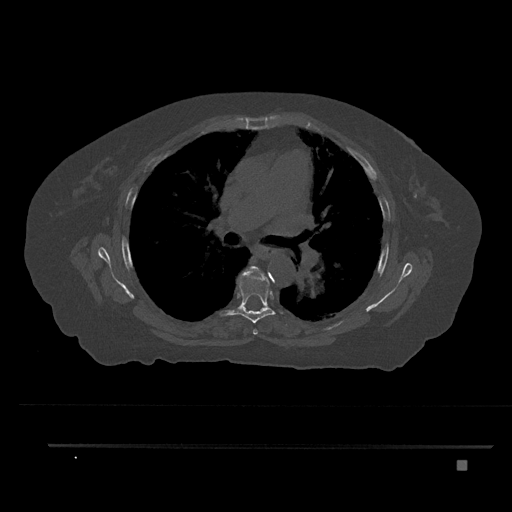
CT including the spine, one axial slice. Position 532 of 797 along the scan axis. Reconstruction kernel Br40s/3. Bone window (W 1800 / L 400 HU). 0.5 mm slice thickness. 512 × 512 image matrix. Female patient, age 76 years. From the clinical record (not read from this slice): primary cancer: lung; vertebrae with lytic lesions (as recorded): T11, L3.
Structures marked on this image (semi-automatically segmented with operator editing):
- T5 vertebra: box from (x=245, y=266) to (x=263, y=335) px
- T6 vertebra: (x=220, y=270)–(x=284, y=323)